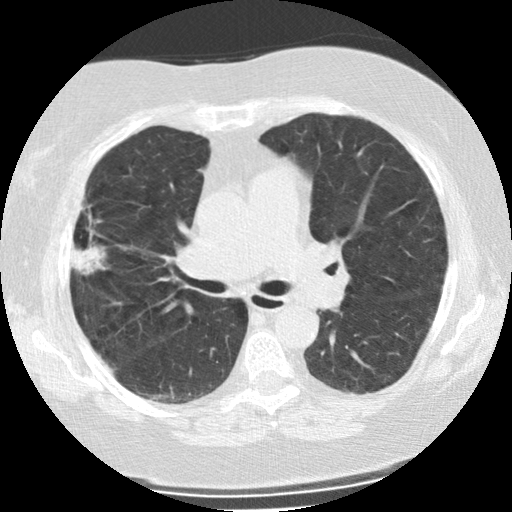
Low-dose screening chest CT, one axial slice. Slice 138 of 225 in the series (ordered by position). Reconstruction kernel STANDARD. 120 kVp. Lung window (W 1500 / L -600 HU). 2.5 mm slice thickness. 512 × 512 image matrix.
Annotated regions visible in this slice (manually delineated by an expert):
- lesion 1 (tumor, upper lobe of right lung): box from (x=71, y=245) to (x=106, y=275) px